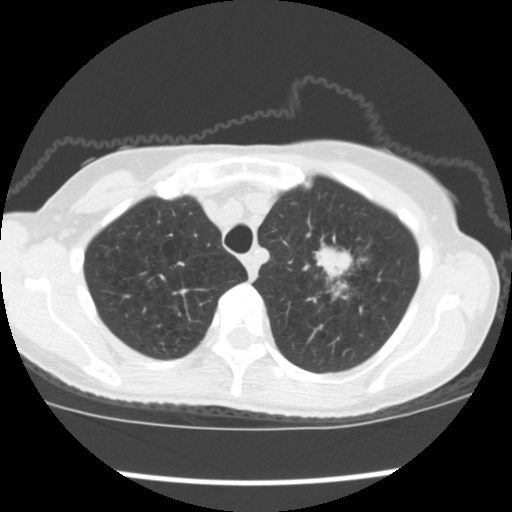
Low-dose screening chest CT, one axial slice. Reconstruction kernel STANDARD. 120 kVp. Lung window (W 1500 / L -600 HU). 2.5 mm slice thickness. 512 × 512 image matrix.
Structures marked on this image (expert manual segmentation):
- lesion 1 (tumor, upper lobe of left lung): bounding box <315,244,353,301> (left, top, right, bottom; pixels)